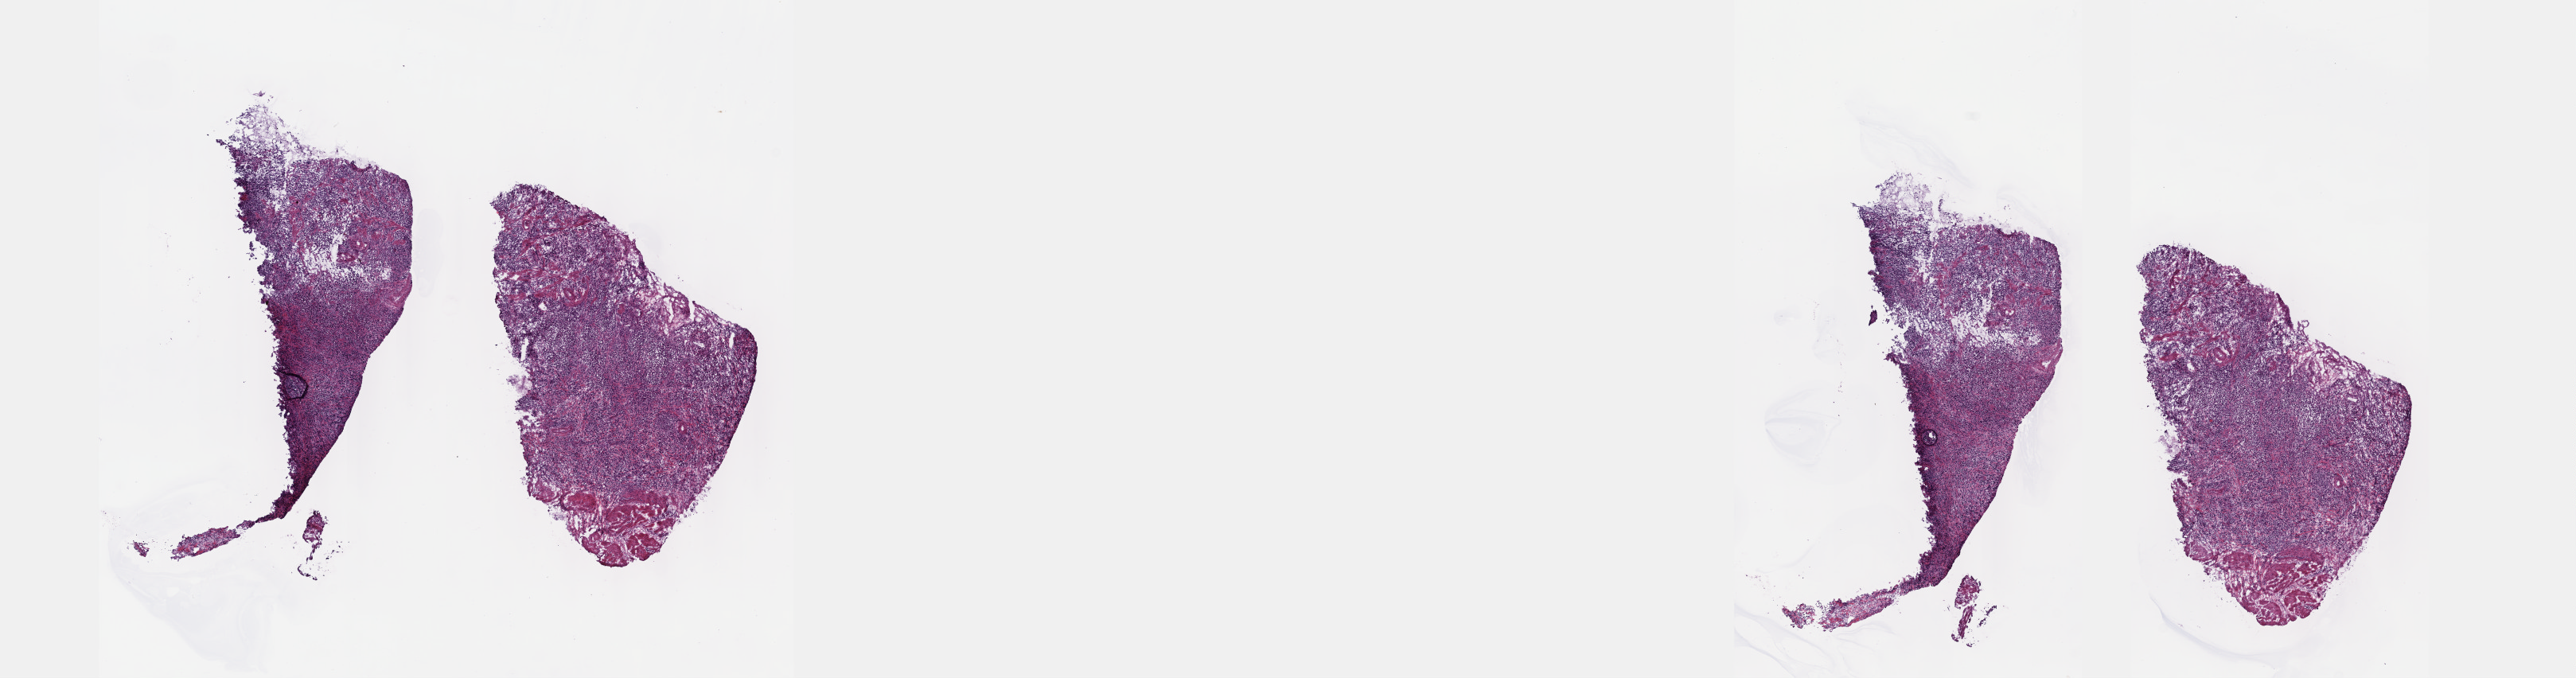
Digitized H&E tissue section (whole slide) — a low-resolution overview of the entire scanned area, about 26.2 x 6.9 mm, frozen section, stomach, primary tumour sample. Female patient; age at initial diagnosis 63 years. Histologic grade: G3 (poorly differentiated). Composition of this section per pathologist review: tumour cells 80%, tumour nuclei 90%, normal cells 10%, stromal cells 10%, necrosis 0%. Inflammatory infiltration, as recorded: lymphocyte infiltration 0%, monocyte infiltration 0%, neutrophil infiltration 0%.
AJCC pathologic stage: II (6th edition). Lymph nodes positive (case pathology): 2 of 4 examined. Histologic diagnosis: Carcinoma, diffuse type.